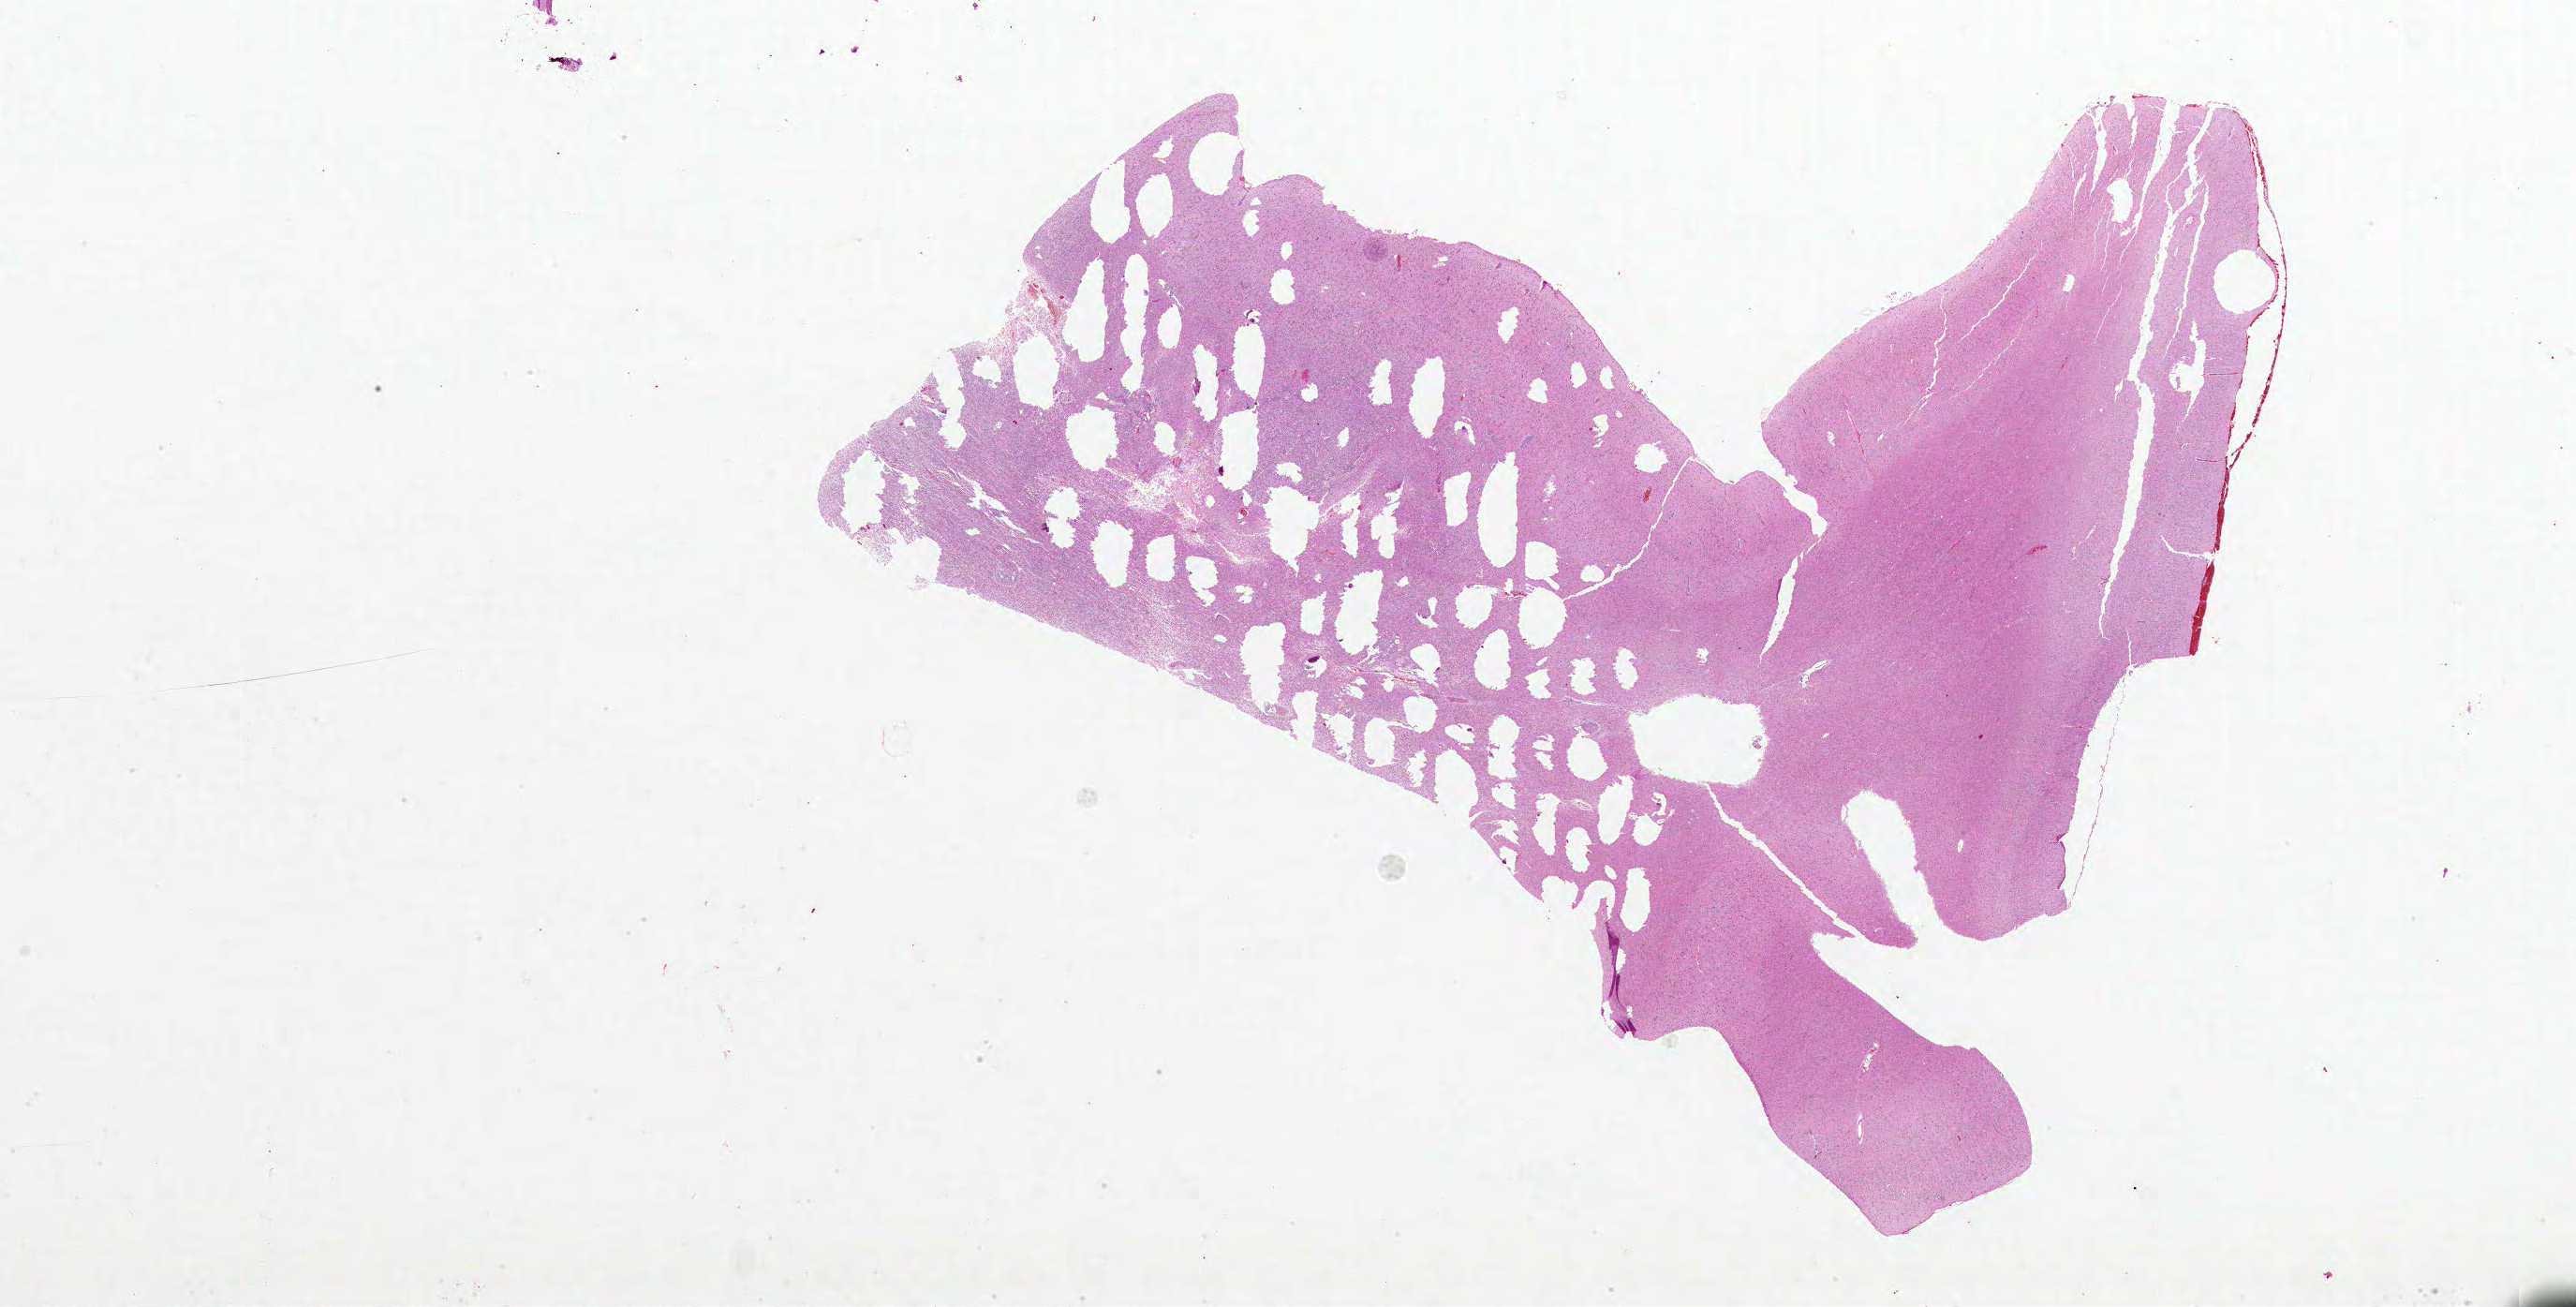
Whole-slide histology image, H&E-stained, a low-resolution overview of the entire scanned area, about 44.0 x 22.3 mm (slide scanned at 20x); formalin-fixed paraffin-embedded (FFPE) diagnostic section; primary tumour sample from the brain. Male patient; age at initial diagnosis 61 years.
• pathologic diagnosis: Glioblastoma